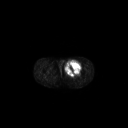
FDG PET of an extremity soft-tissue mass (from a PET/CT study), one axial slice. 128 × 128 image matrix. Patient: male, 63 years. Case-level facts recorded for this patient, not image findings: histological type: pleiomorphic liposarcoma; grade: high; site of the primary tumour: left thigh.
Structures marked on this image (expert contour drawn on MRI and transferred to this co-registered scan by the dataset authors):
- gross tumour volume including surrounding oedema: bounding box [x1, y1, x2, y2] px = [65, 60, 82, 75]
- gross tumour volume (mass): [65, 60, 81, 75]